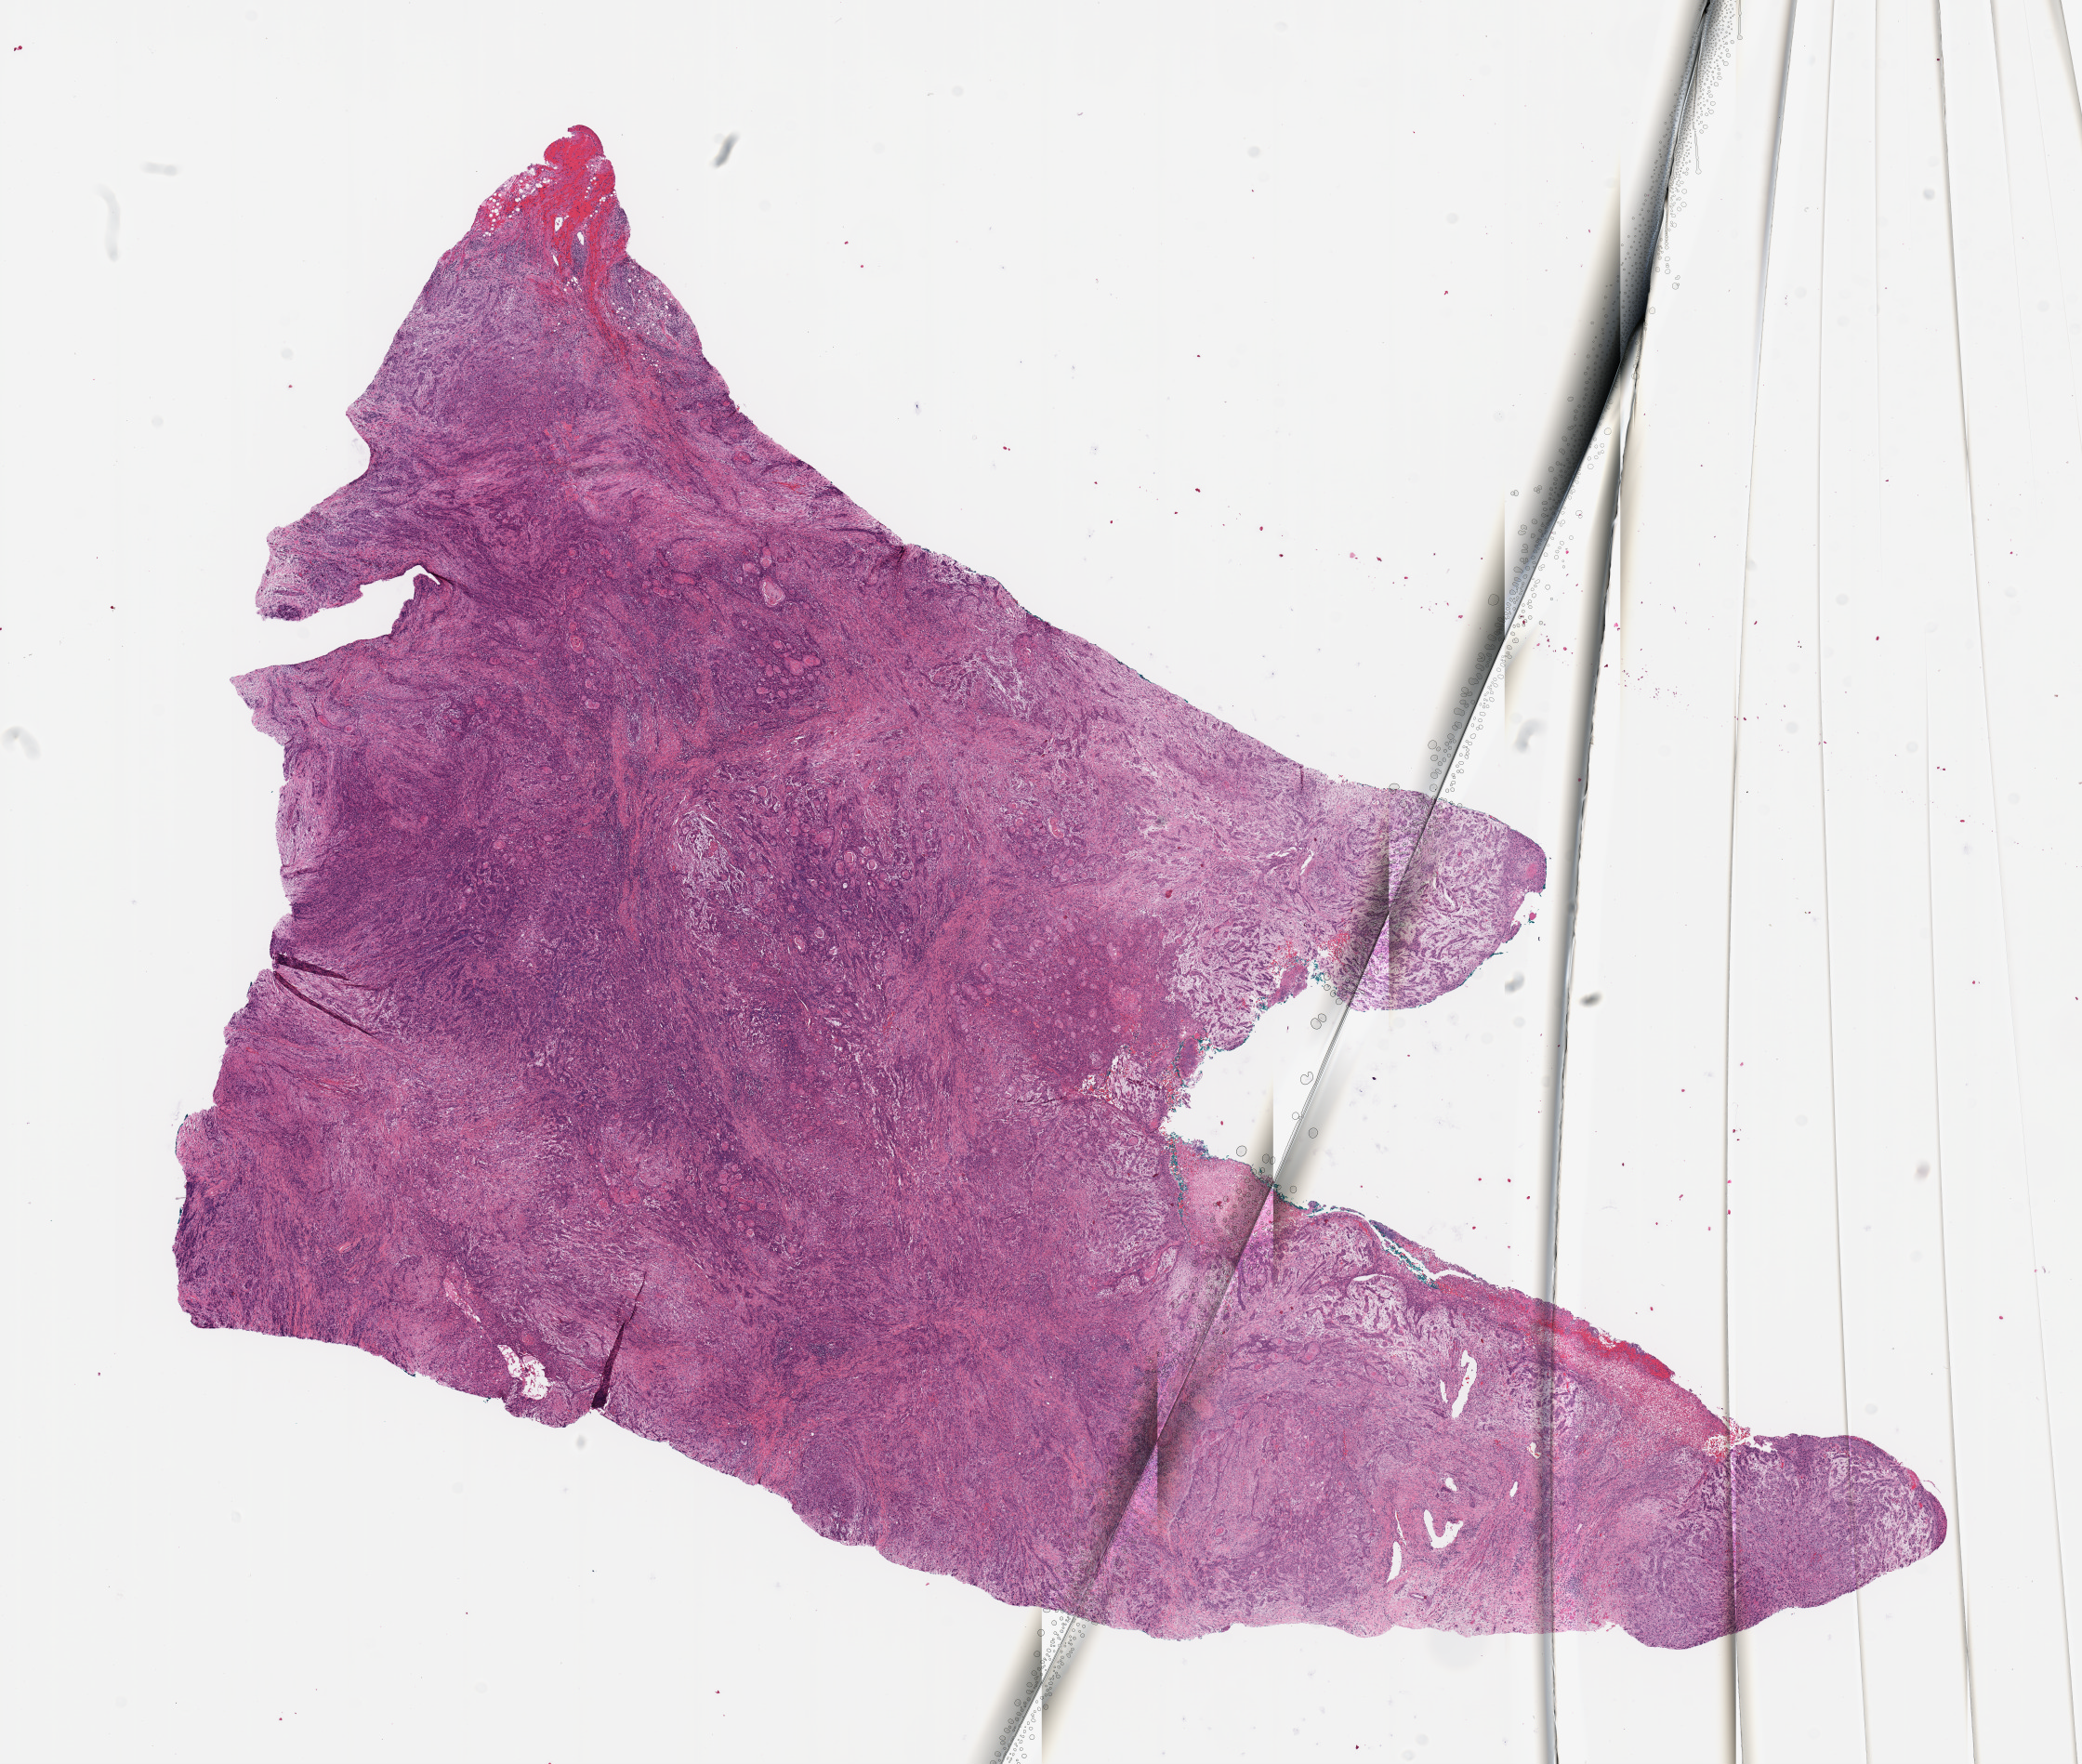
Whole-slide histology image, H&E-stained — shown as a low-resolution overview of the whole scanned area (about 17.7 x 15.0 mm). Tumour tissue sample, sampled site: tongue. Patient: male, age 50 years. Slide review estimates, as recorded: tumour nuclei 80%, necrosis 5%.
Diagnosis: Squamous cell carcinoma, NOS (tongue, NOS).